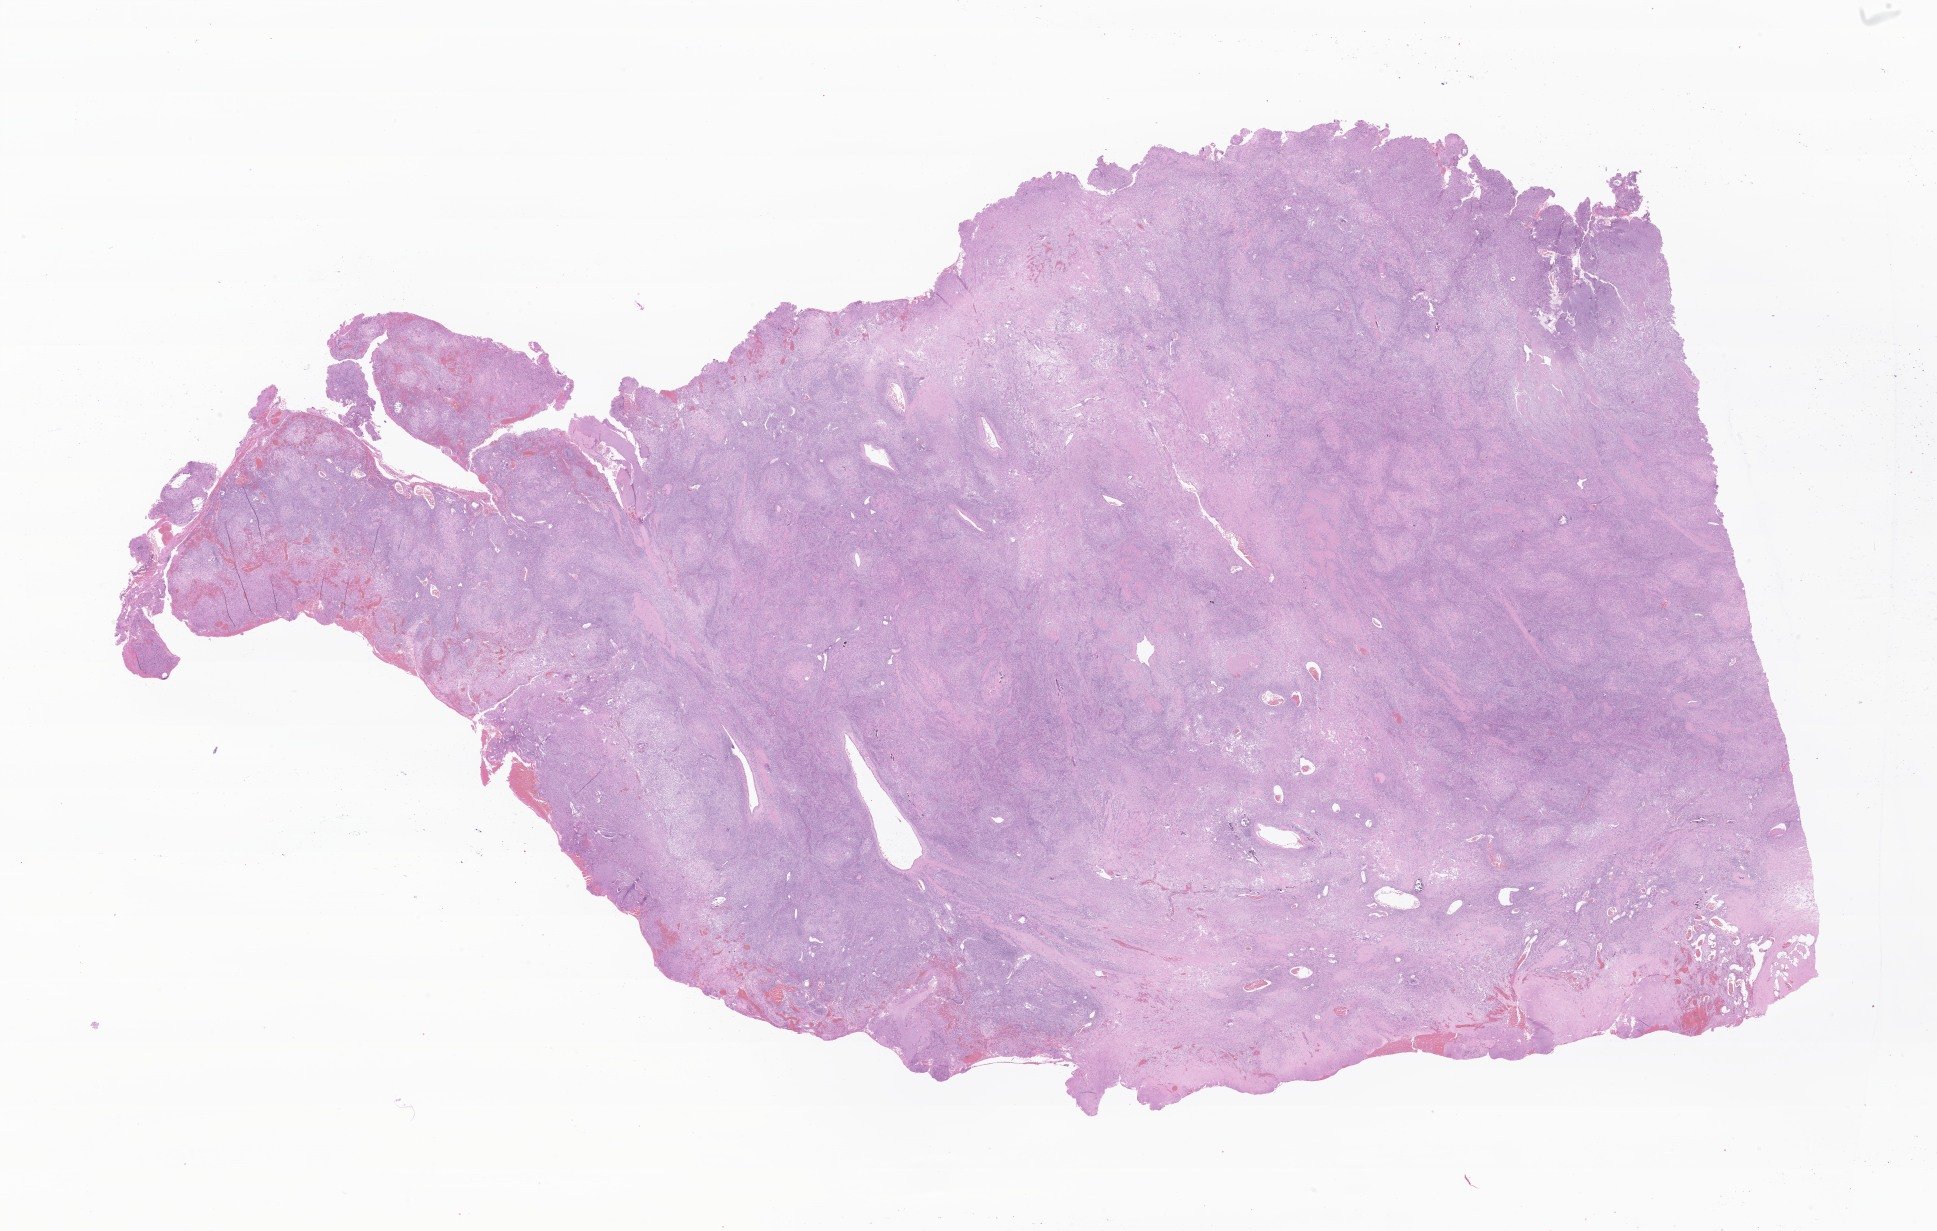
Hematoxylin and eosin (H&E) whole-slide image of tumor tissue from the brain — a low-resolution overview of the entire scanned area, about 32.7 x 20.8 mm. Formalin-fixed paraffin-embedded section. Patient male; age 171 months (14 years 3 months).
Diagnosis: Meningioma, NOS.